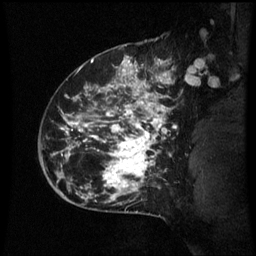
Breast MRI (dynamic contrast-enhanced), one sagittal slice. Dynamic contrast-enhanced series, image 2 of 3 at this slice position (ordered by acquisition). 1.5 T. TE 4.2 ms, TR 8.9 ms. 256 × 256 image matrix, field of view 200 × 200 mm. Female patient, age 42 years. From the clinical record (not read from this slice): setting: breast cancer imaged before/during neoadjuvant chemotherapy; receptor status: HER2-positive.
Structures marked on this image (semi-automatic segmentation, software-assisted and operator-edited):
- analysis volume of interest (the breast-tissue region the enhancement analysis was run in; not a lesion): bounding box [x1, y1, x2, y2] px = [66, 82, 173, 193]
- tumour enhancement mask (voxels above the 70 % enhancement threshold inside the analysis volume of interest): [66, 82, 171, 191]